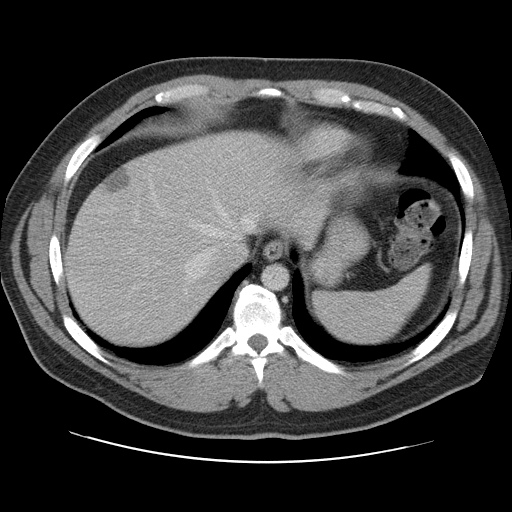
Contrast-enhanced abdominal CT, one axial slice. Position 91 of 109 along the scan axis. 120 kVp. Intravenous contrast given. Soft-tissue window (W 400 / L 40 HU). 512 × 512 image matrix, field of view 402 × 402 mm. Male patient, age 35 years. Case-level facts recorded for this patient, not image findings: diagnosis: colorectal cancer liver metastases, imaged before liver resection; multiple liver metastases: yes.
Annotated regions visible in this slice (outlined manually by an expert reader):
- hepatic veins: bounding box <142,182,257,319> (left, top, right, bottom; pixels)
- liver: <66,131,325,347>
- planned liver remnant (the part of the liver to remain after resection): <66,131,325,347>
- liver metastasis: <104,170,131,193>